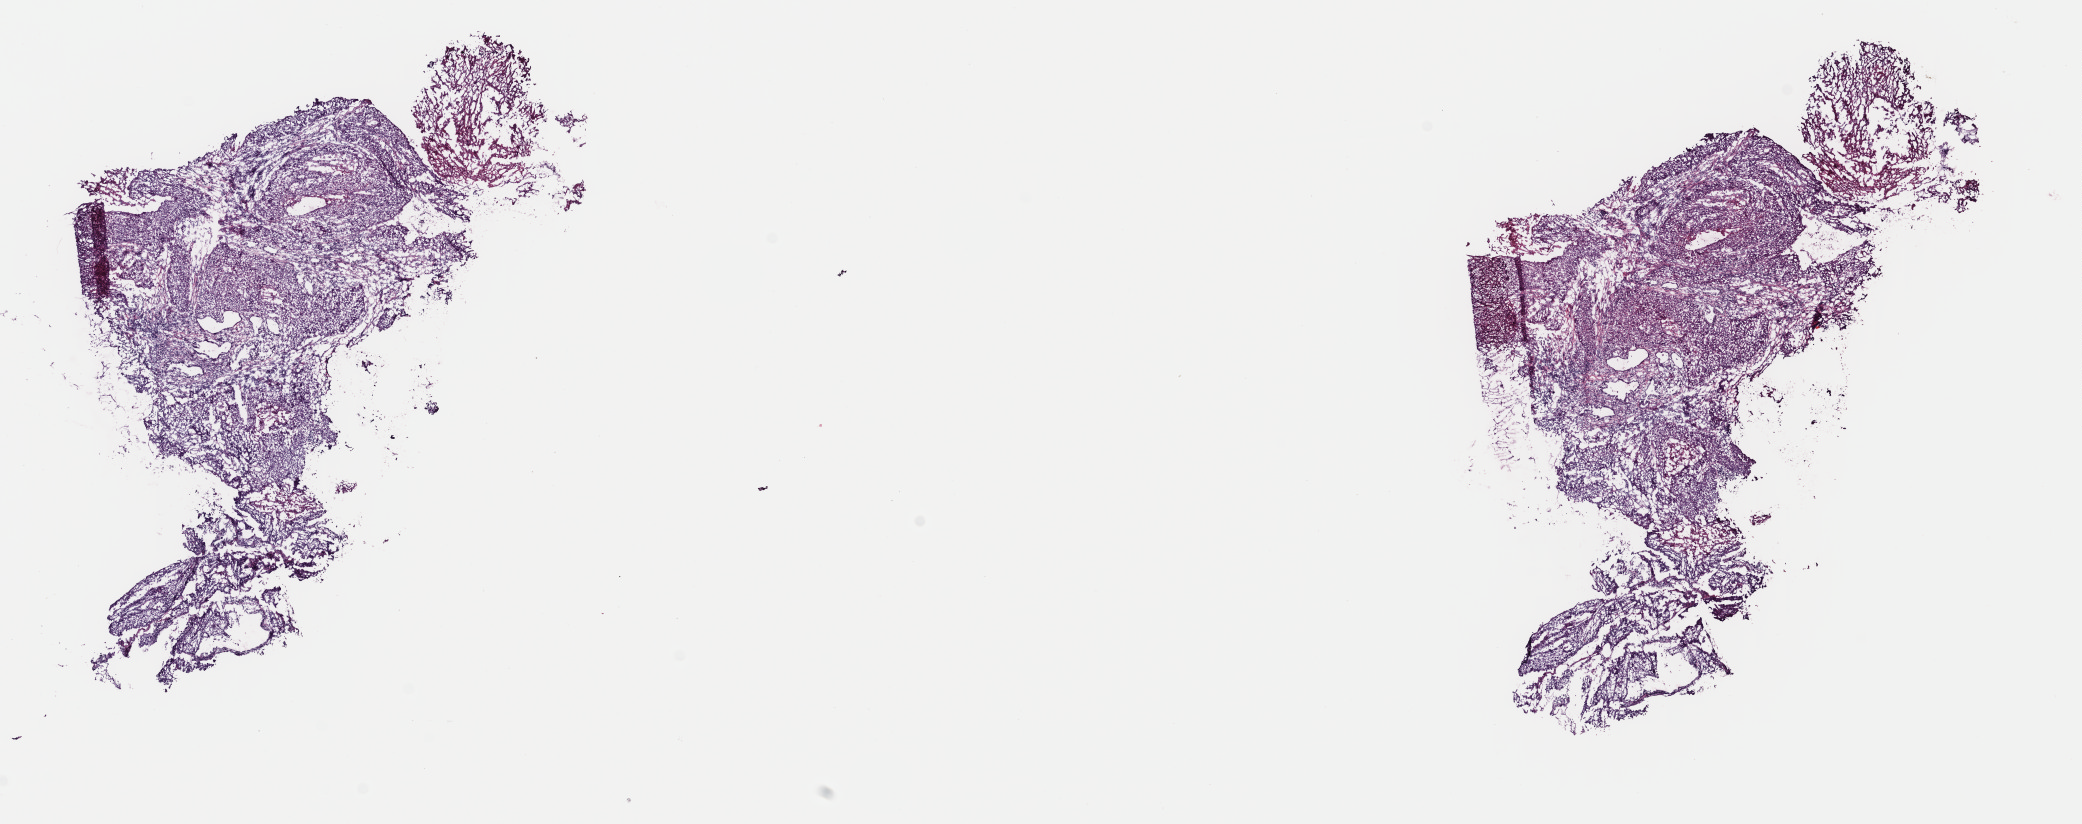
Hematoxylin and eosin (H&E) stained whole-slide image — shown as a low-resolution overview of the whole scanned area (about 16.4 x 6.5 mm), frozen section from the top of the tissue portion, sample: primary tumour, cervix. Female, age 37 years at initial diagnosis. Histologic grade: GX (grade cannot be assessed). Pathologist review of this section (percent, as recorded): tumour cells 70%, tumour nuclei 70%, normal cells 0%, stromal cells 20%, necrosis 10%. Infiltration values recorded for this section: lymphocyte infiltration 40%, monocyte infiltration 20%, neutrophil infiltration 20%.
FIGO stage: IB2. Histologic diagnosis: Squamous cell carcinoma, large cell, nonkeratinizing, NOS (cervix uteri).